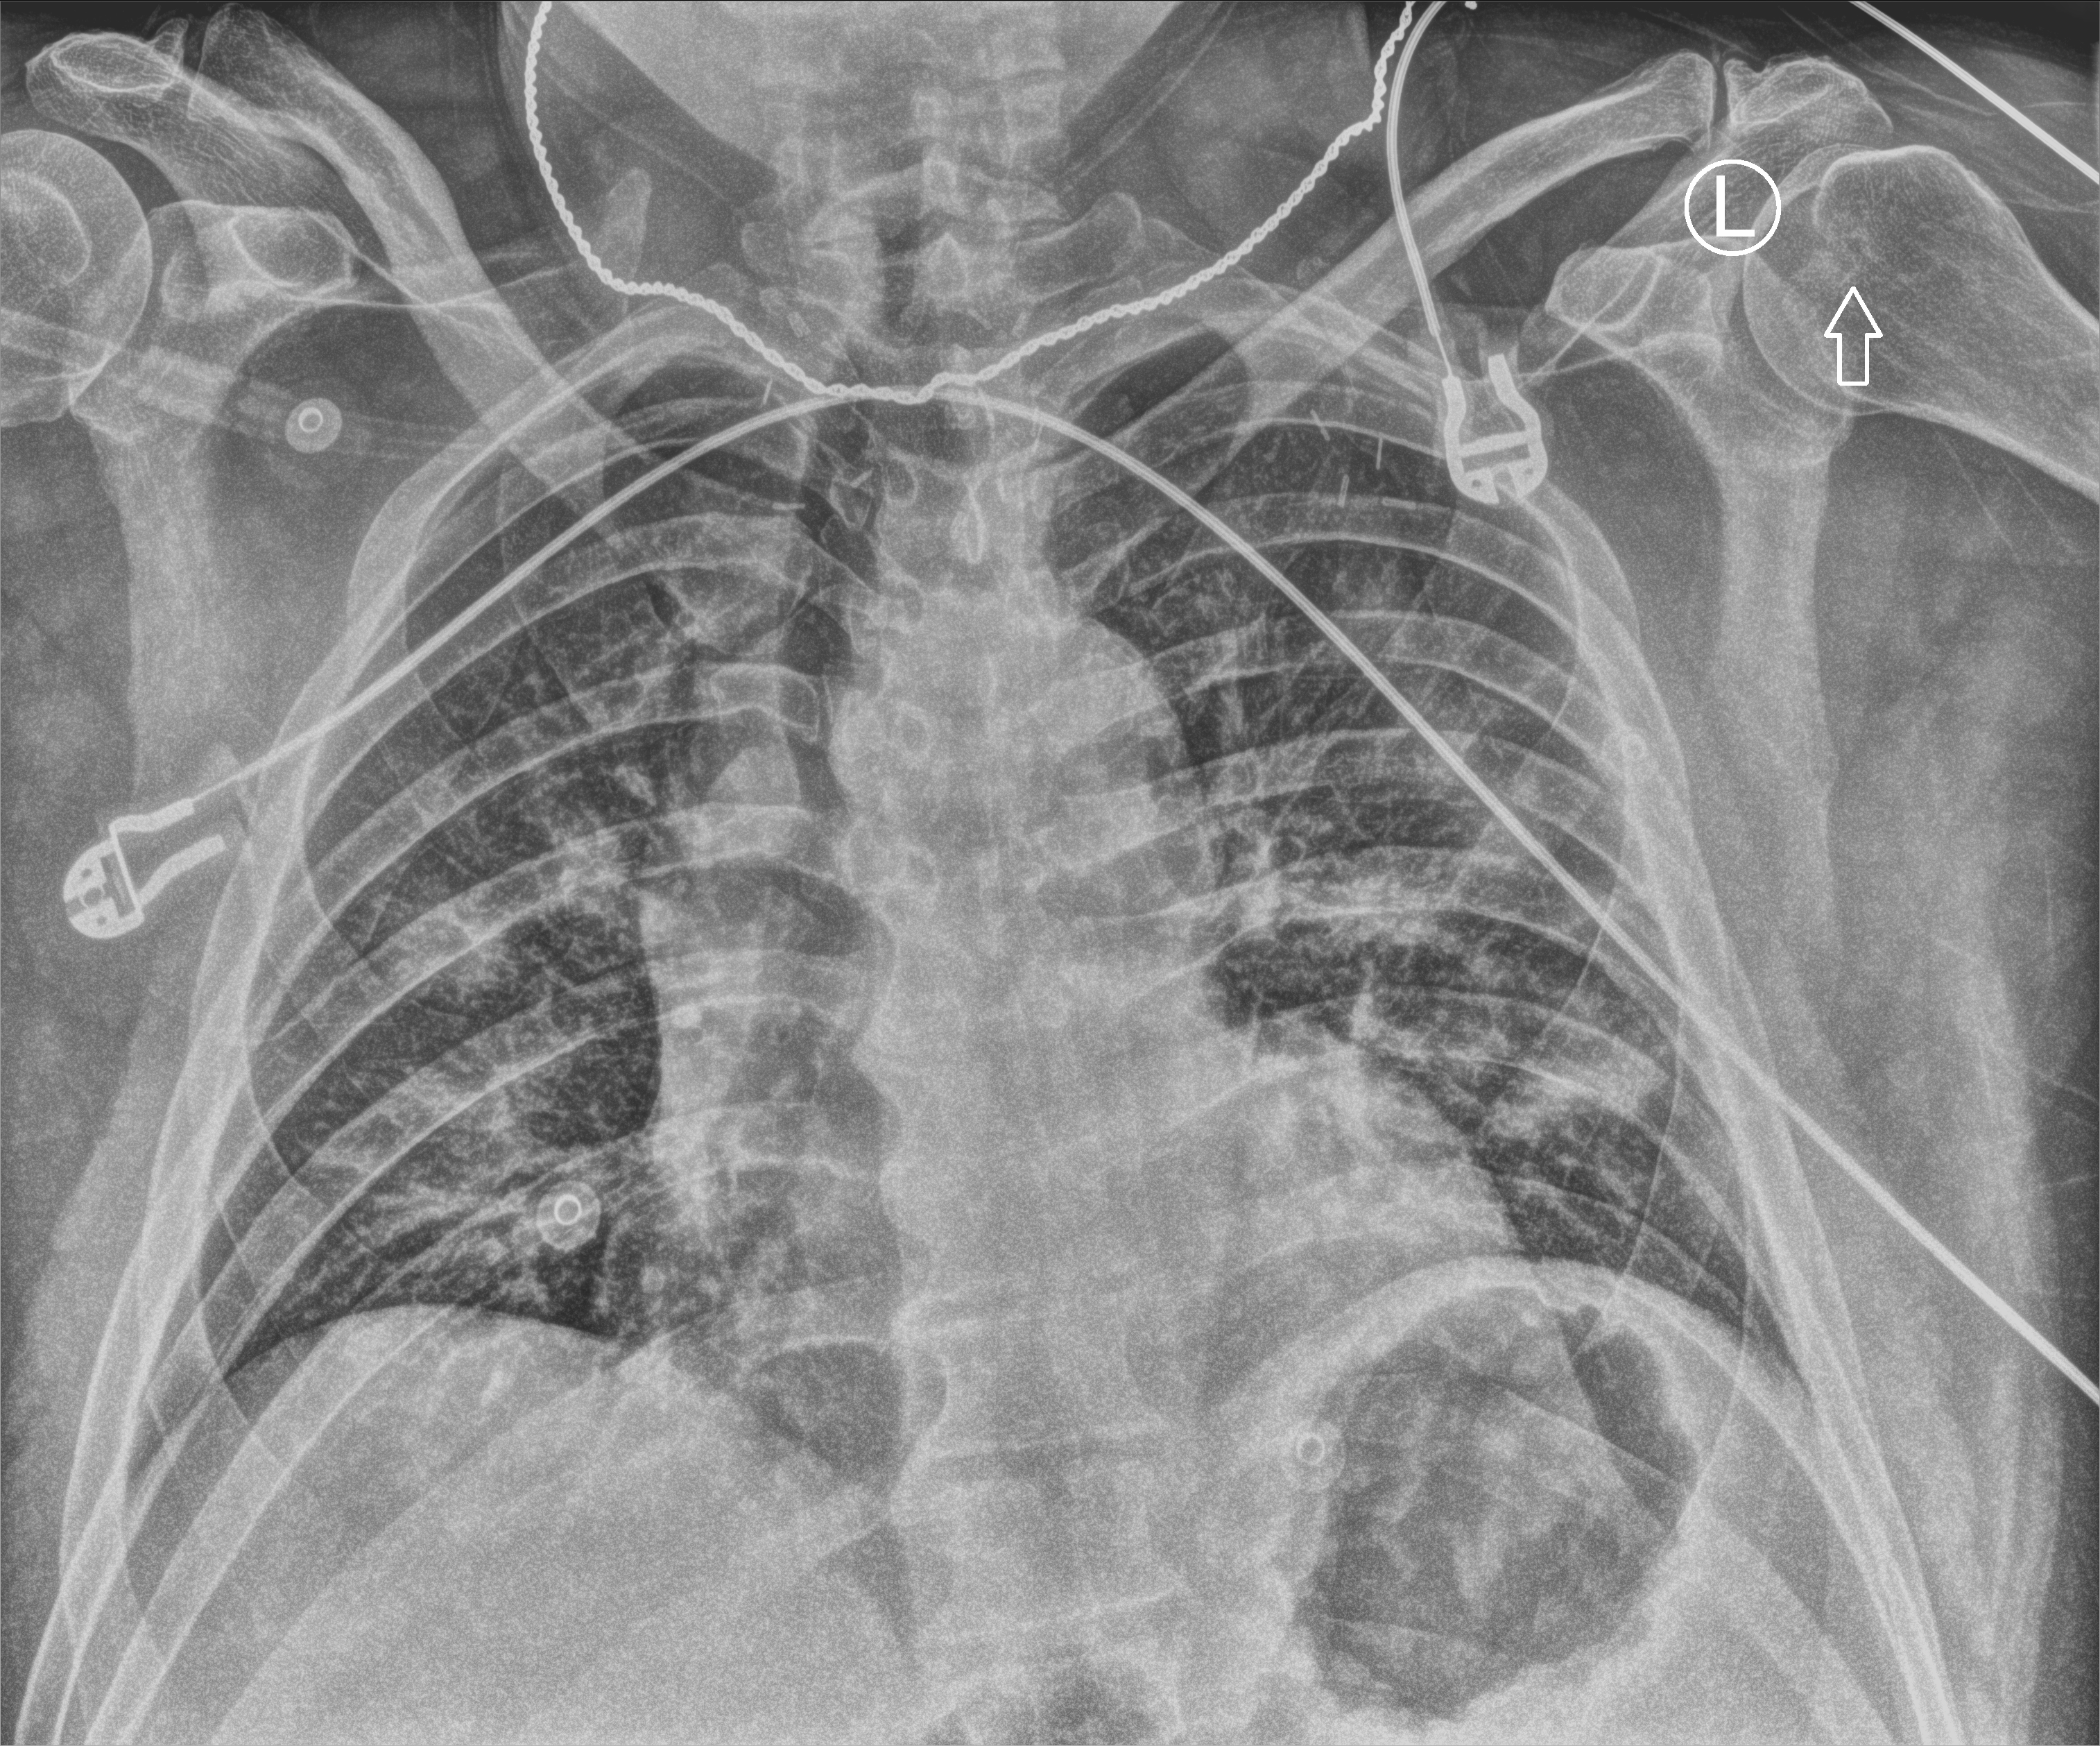
Bedside chest radiograph (computed radiography). Adult patient hospitalised with COVID-19, age 18–59 years.
Admission-level facts for this patient (not findings on this image; timing relative to this image not recorded):
- mechanically ventilated during this hospital stay: yes
- admitted to intensive care during this hospital stay: yes
- hypertension (admission record): no